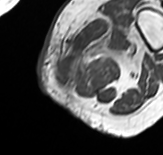
MRI of an extremity soft-tissue mass, one axial slice; slice 13 of 65 in the series (ordered by position); MR volume resampled by the dataset authors to the PET/CT grid (not the native acquisition matrix); 163 × 155 image matrix. Female patient. Case-level facts recorded for this patient, not image findings: histological type: pleomorphic leiomyosarcoma; grade: high; site of the primary tumour: left thigh.
Annotated regions visible in this slice (expert contour drawn on MRI and transferred to this co-registered scan by the dataset authors):
- gross tumour volume including surrounding oedema: bounding box (x1, y1, x2, y2) in pixels: (57, 19, 143, 87)
- gross tumour volume (mass): (58, 72, 79, 86)